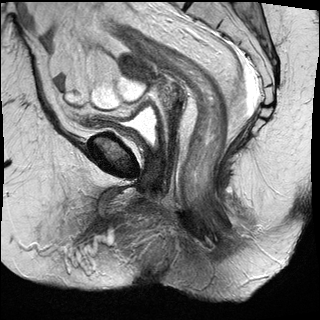
Pelvic MRI for cervical cancer, one sagittal slice; position 15 of 27 along the scan axis; T2-weighted; 1.5 T; TE 89 ms, TR 2740 ms; 320 × 320 image matrix, field of view 260 × 260 mm. Female patient, age 67 years.
Structures marked on this image (expert manual segmentation):
- uterus and cervix: box from (x=117, y=52) to (x=162, y=85) px